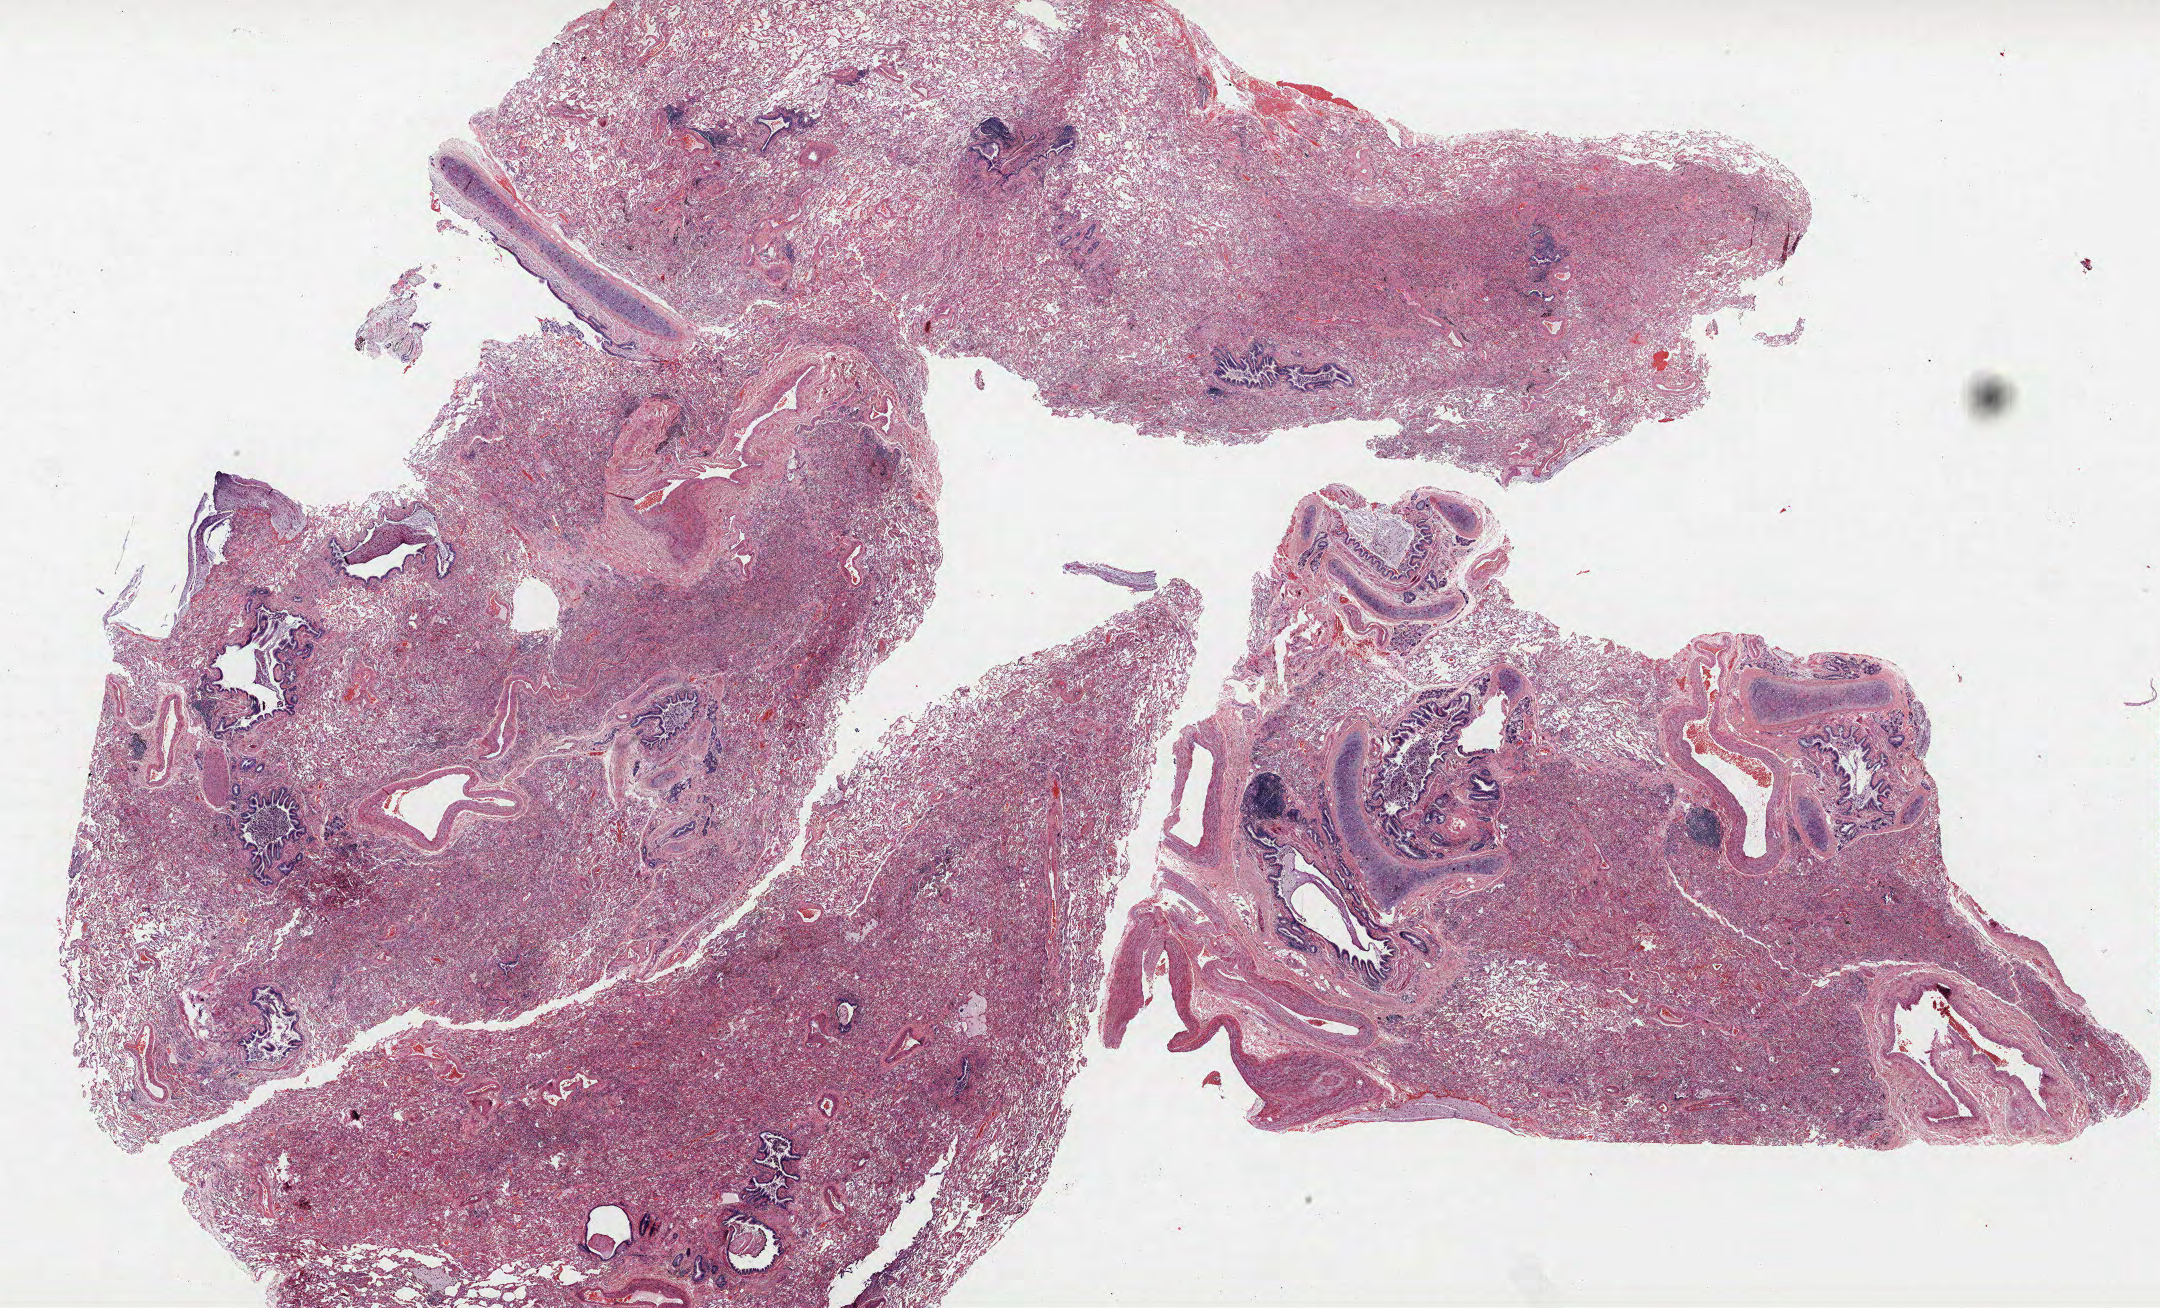
Whole-slide histology image, H&E-stained, low-resolution overview of the scanned area, about 34.6 x 20.9 mm (from a 40x scan). FFPE section. Lung. Female, age 59 at enrolment. Current smoker at enrolment.
Participant's lung-cancer diagnosis: Squamous cell carcinoma, NOS (ICD-O-3 8070/3).